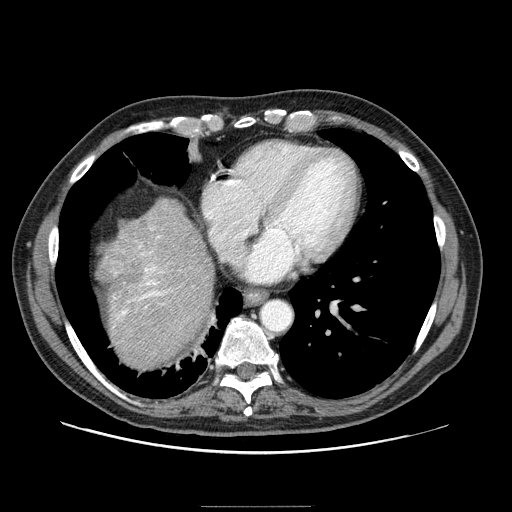
Contrast-enhanced abdominal CT (liver protocol), one axial slice. Reconstruction kernel STANDARD. One of 2 acquisitions stored at this slice position. Soft-tissue window (W 400 / L 40 HU). 2.5 mm slice thickness. 512 × 512 image matrix. From the clinical record (not read from this slice): diagnosis: hepatocellular carcinoma (patient treated with transarterial chemoembolisation; whether this scan precedes or follows treatment is not stated here); TNM stage (as recorded): Stage-II; Child-Pugh class: A; tumour differentiation: well differentiated.
Annotated regions visible in this slice (semi-automatic segmentation, software-assisted and operator-edited):
- liver parenchyma outside the tumour (the mass and vessels are separate outlines, so this box may not span the whole liver): bounding box [x1, y1, x2, y2] px = [100, 198, 212, 368]
- liver vessels: [113, 228, 172, 327]